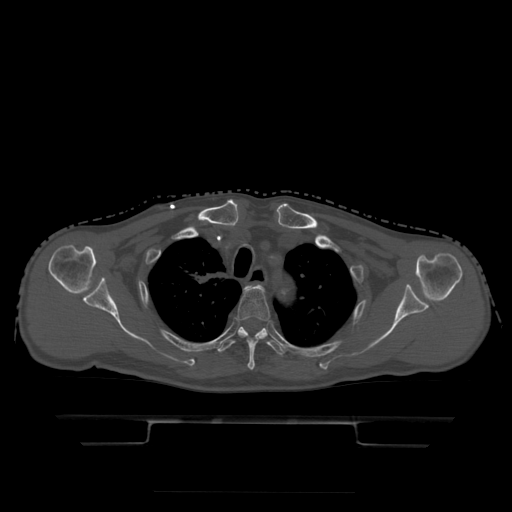
CT including the spine, one axial slice; slice 365 of 522 in the series (ordered by position); bone window (W 1800 / L 400 HU); 1.25 mm slice thickness; 512 × 512 image matrix, field of view 436 × 436 mm. Patient age 68 years. From the clinical record (not read from this slice): primary cancer: urothelial.
Structures marked on this image (semi-automatic segmentation, software-assisted and operator-edited):
- T3 vertebra: box from (x=236, y=285) to (x=271, y=371) px
- T4 vertebra: (x=217, y=327)–(x=286, y=356)